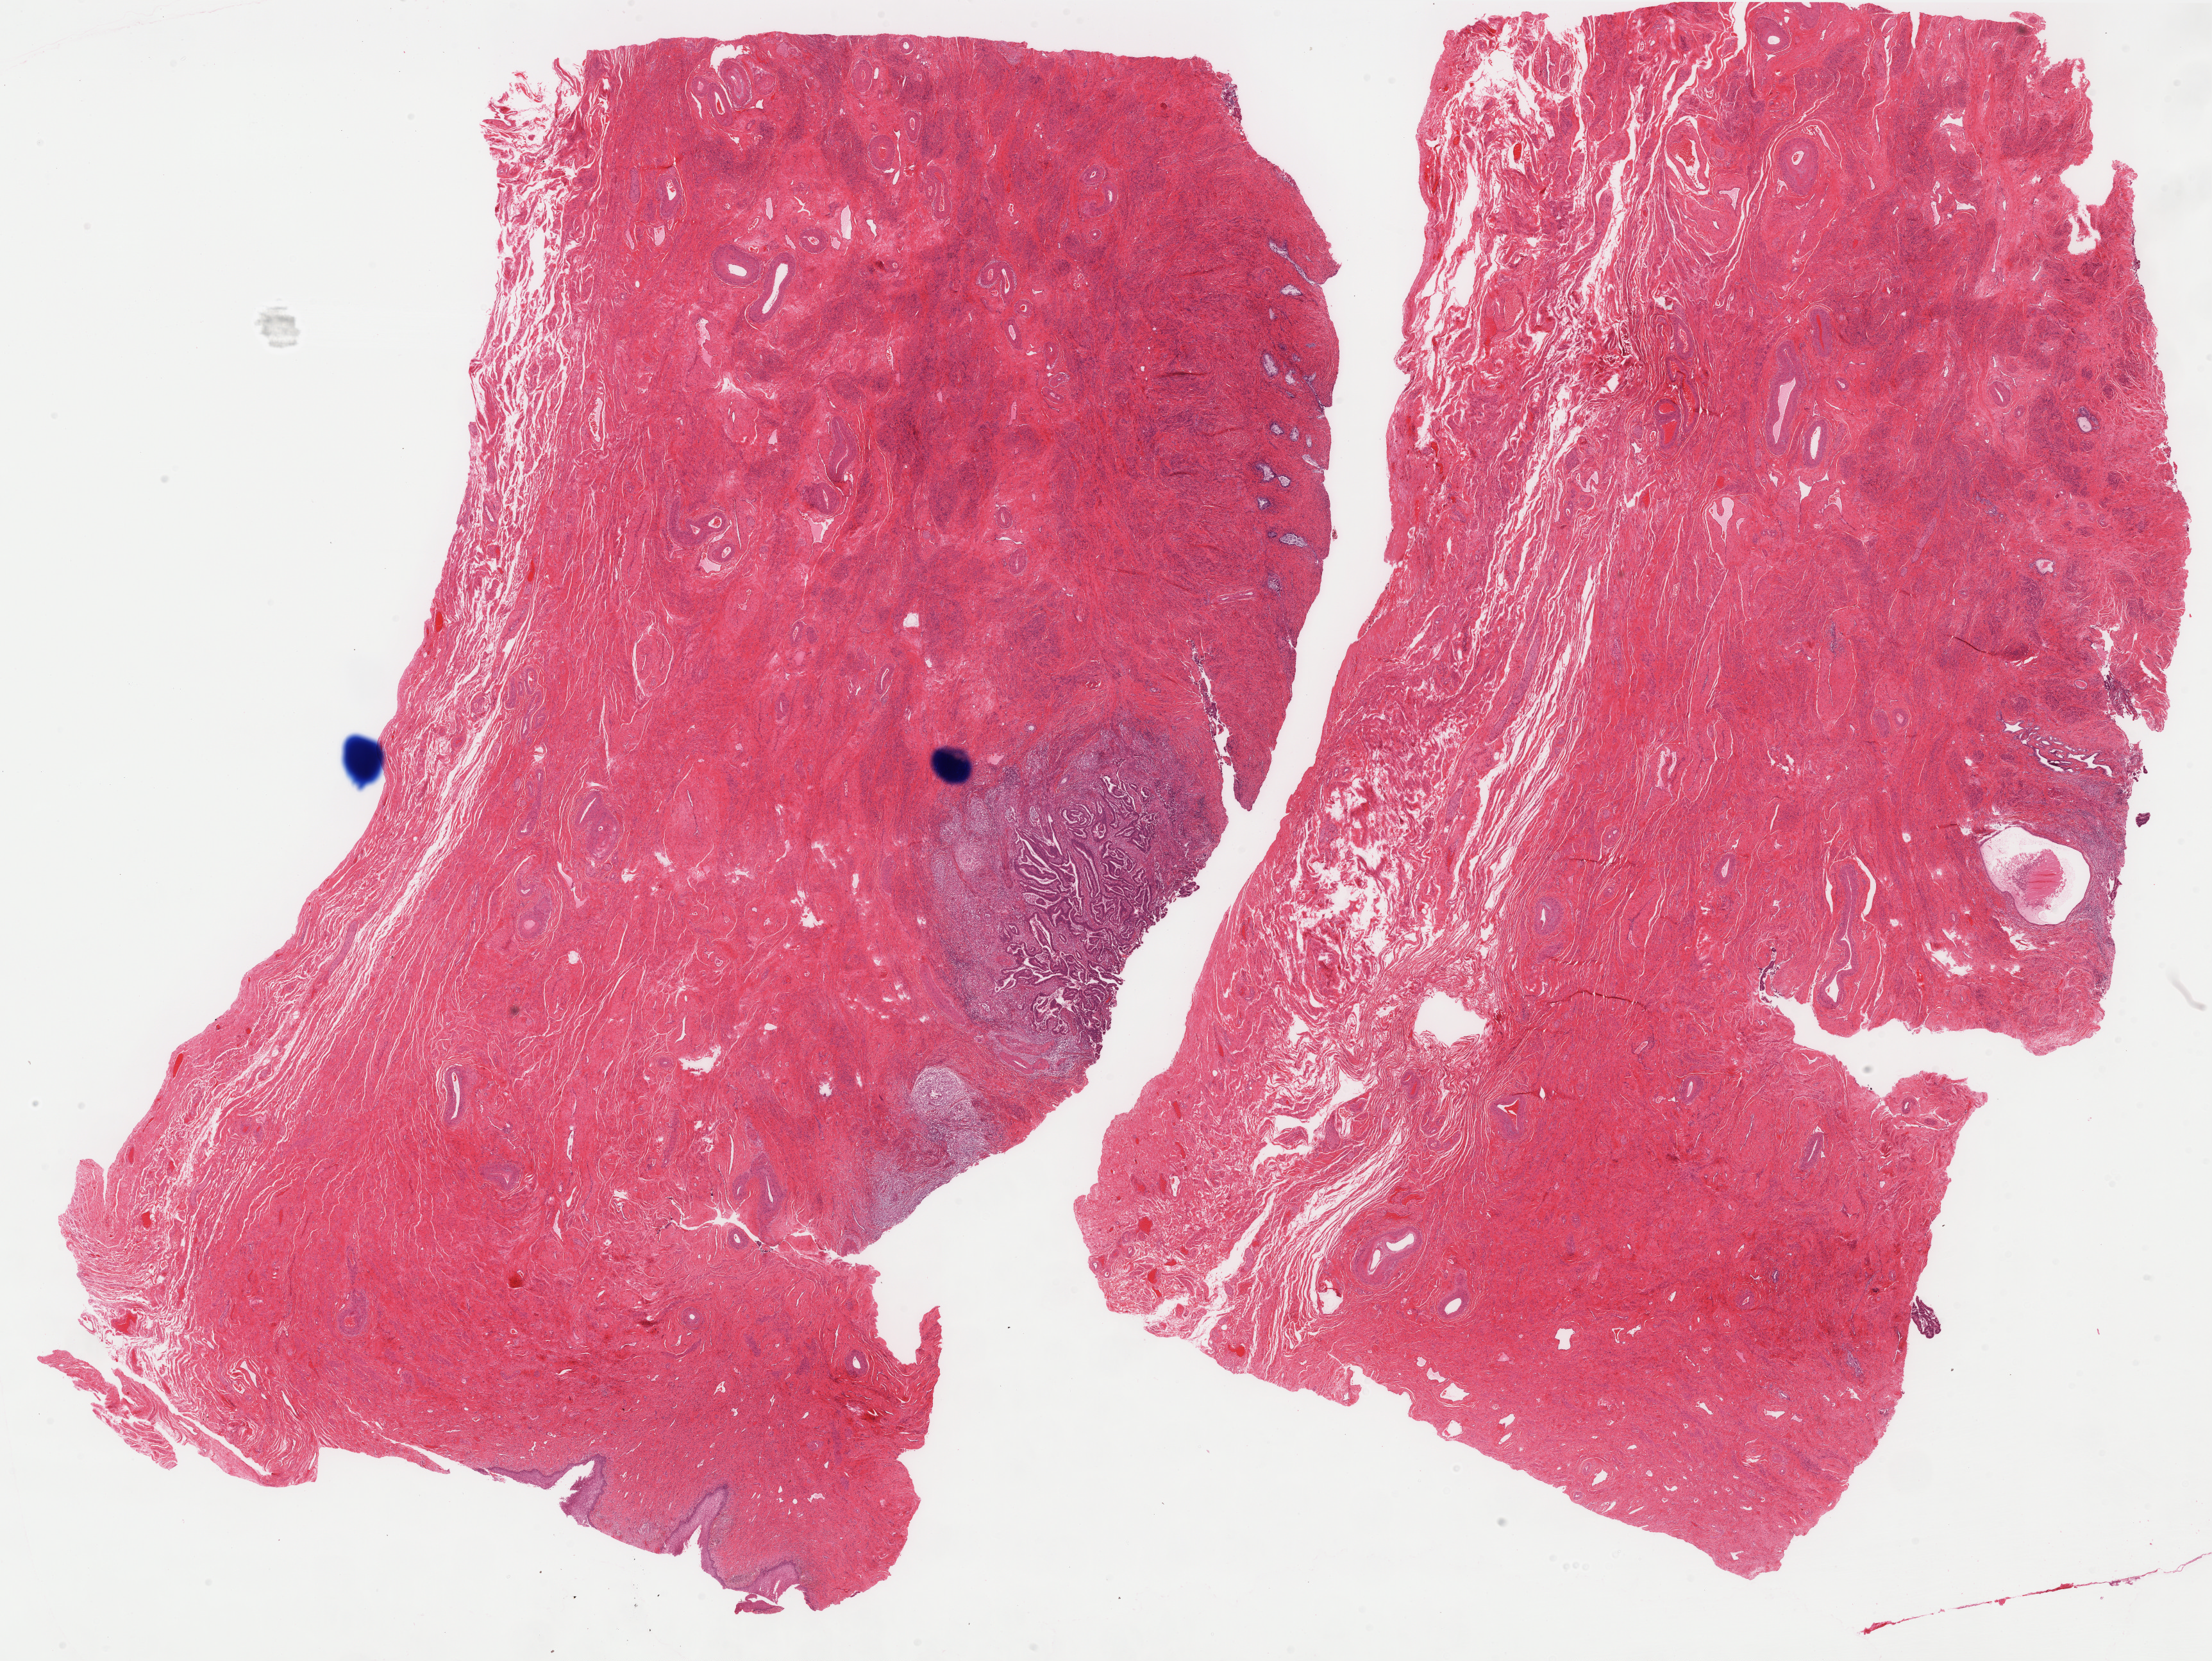
Whole-slide histology image, H&E-stained, low-resolution overview of the scanned area, about 27.6 x 20.7 mm (slide scanned at 40x). Formalin-fixed paraffin-embedded (FFPE) diagnostic section. Primary tumour sample from the cervix. Female, age 61 years at initial diagnosis. Histologic grade: G2 (moderately differentiated).
FIGO stage: IB1. Lymph nodes positive (case pathology): 0 of 18 examined. Pathologic diagnosis: Adenocarcinoma, NOS (cervix uteri).